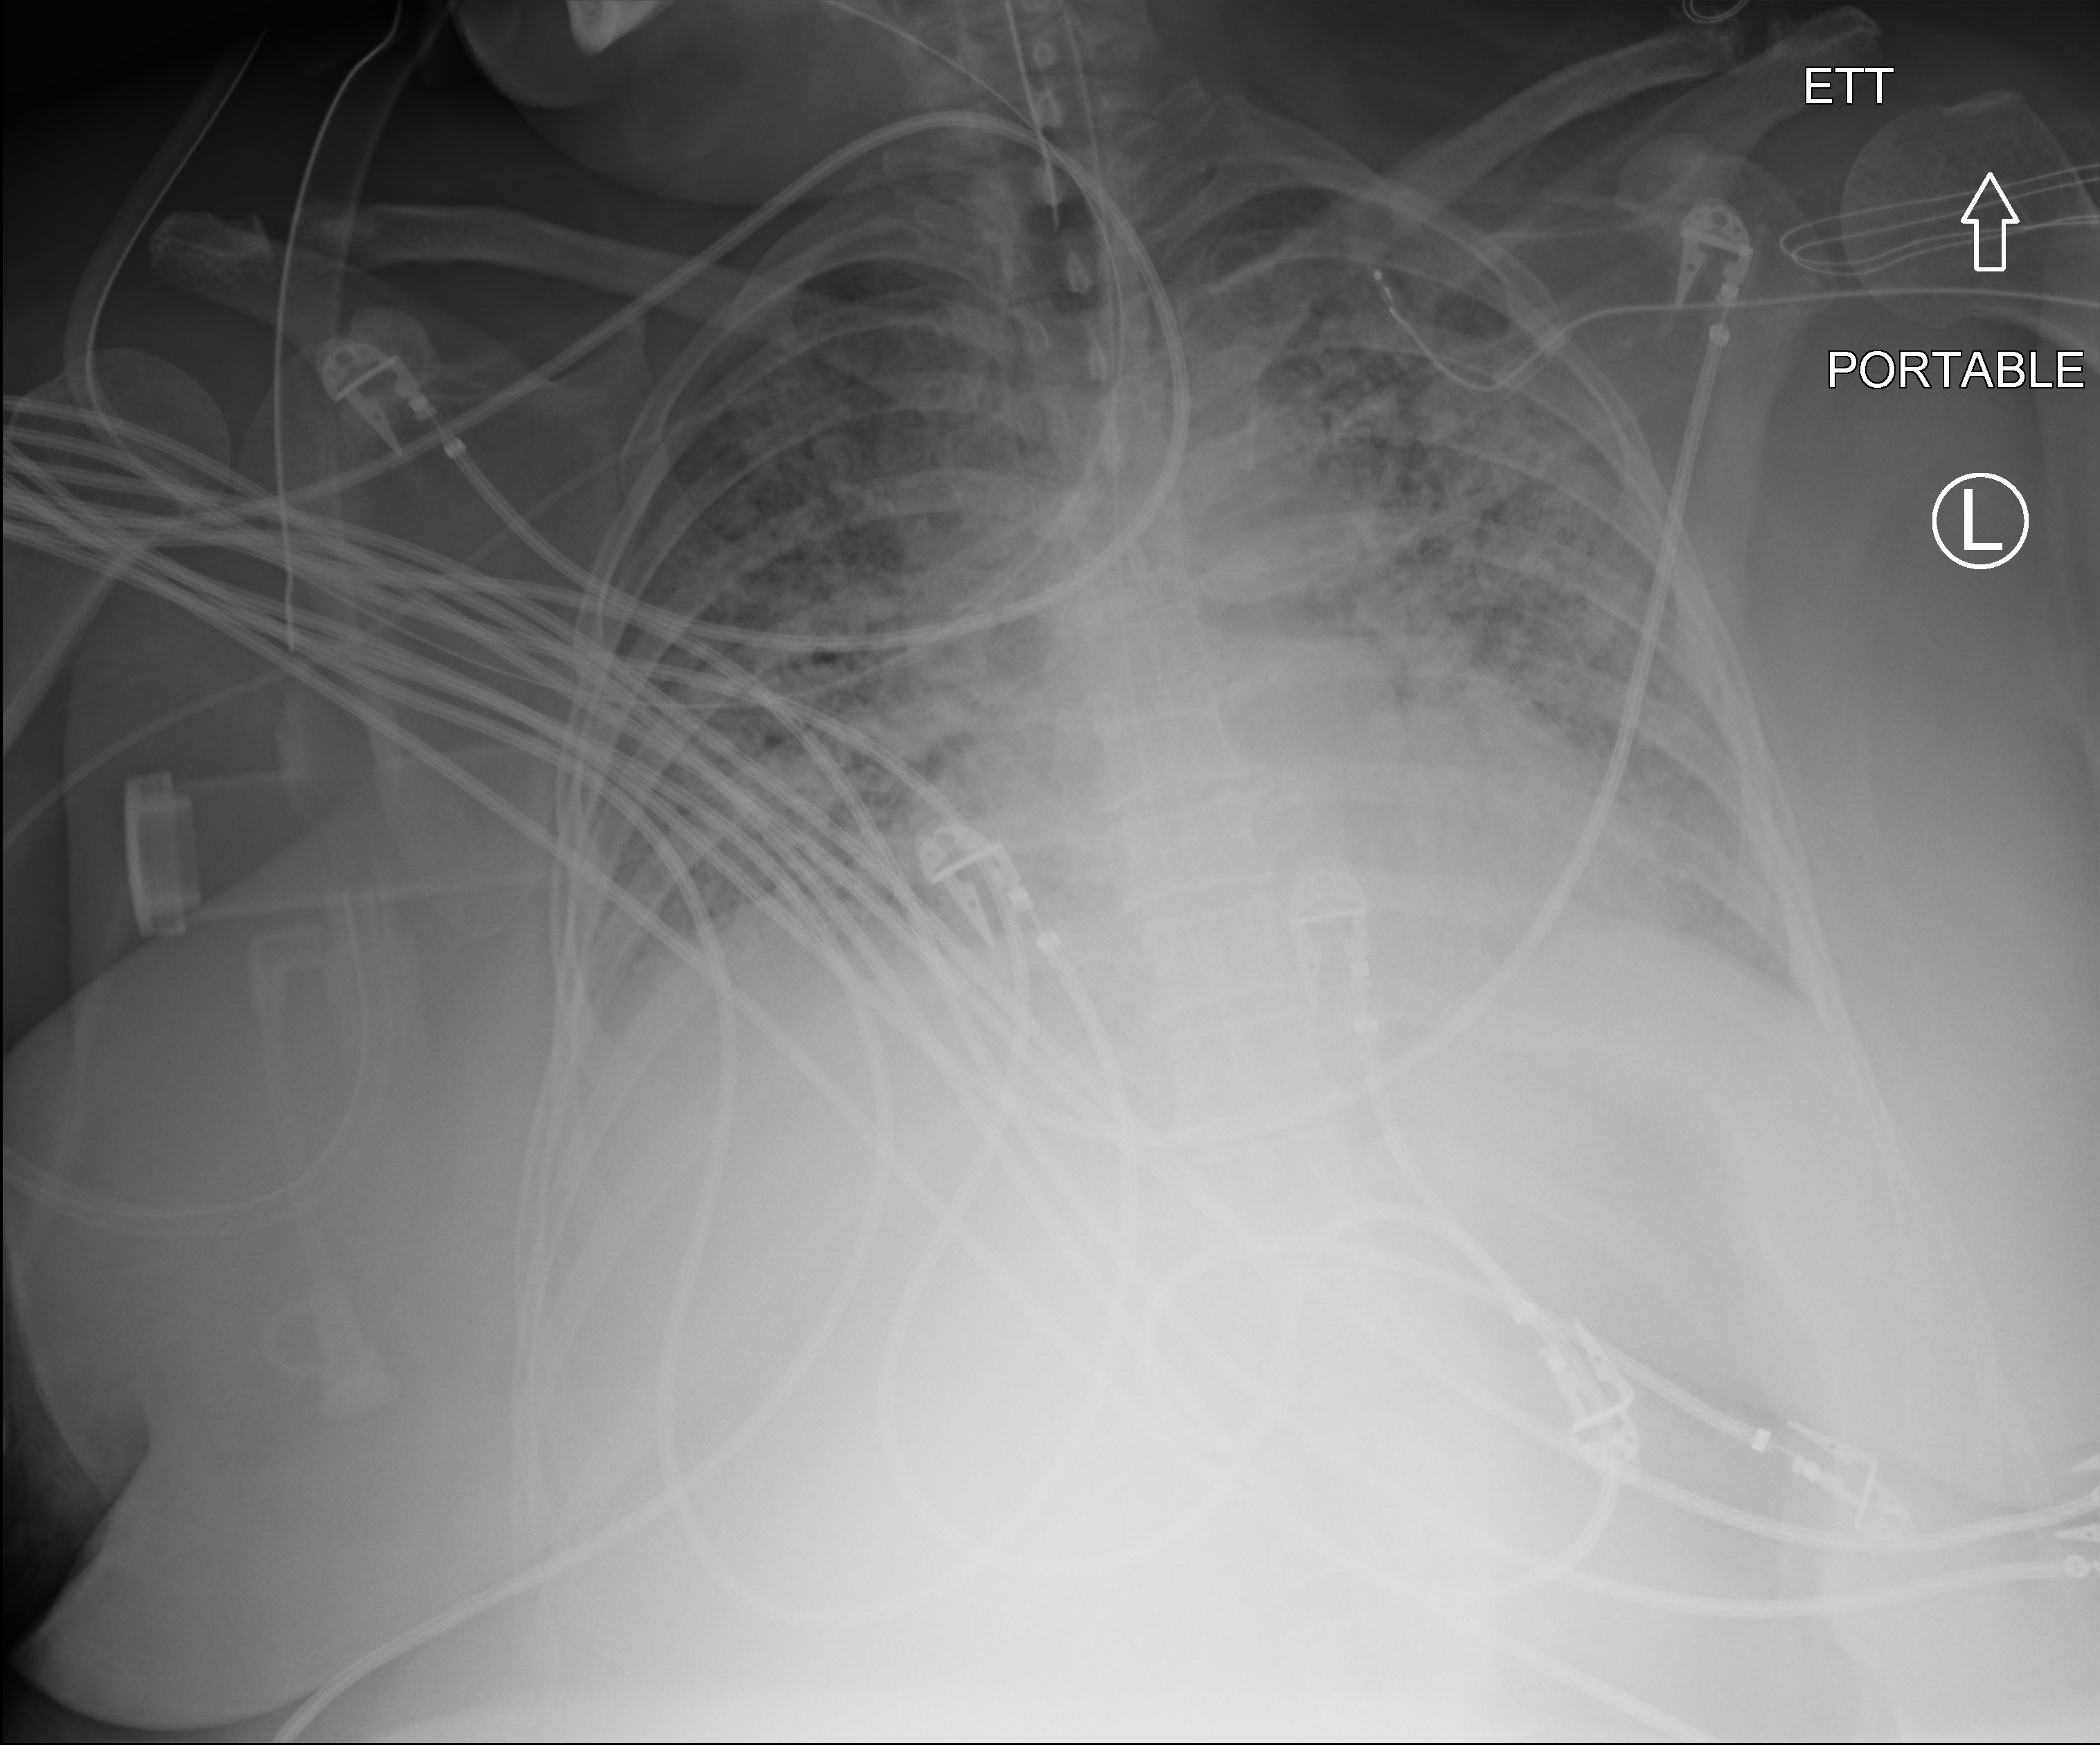
Bedside chest radiograph (computed radiography), anteroposterior (AP) projection. Patient hospitalised with COVID-19; female, aged 18–59 years.
Hospital-stay facts (about this admission, not read from this image; timing relative to this image not recorded):
- mechanically ventilated during this hospital stay: yes